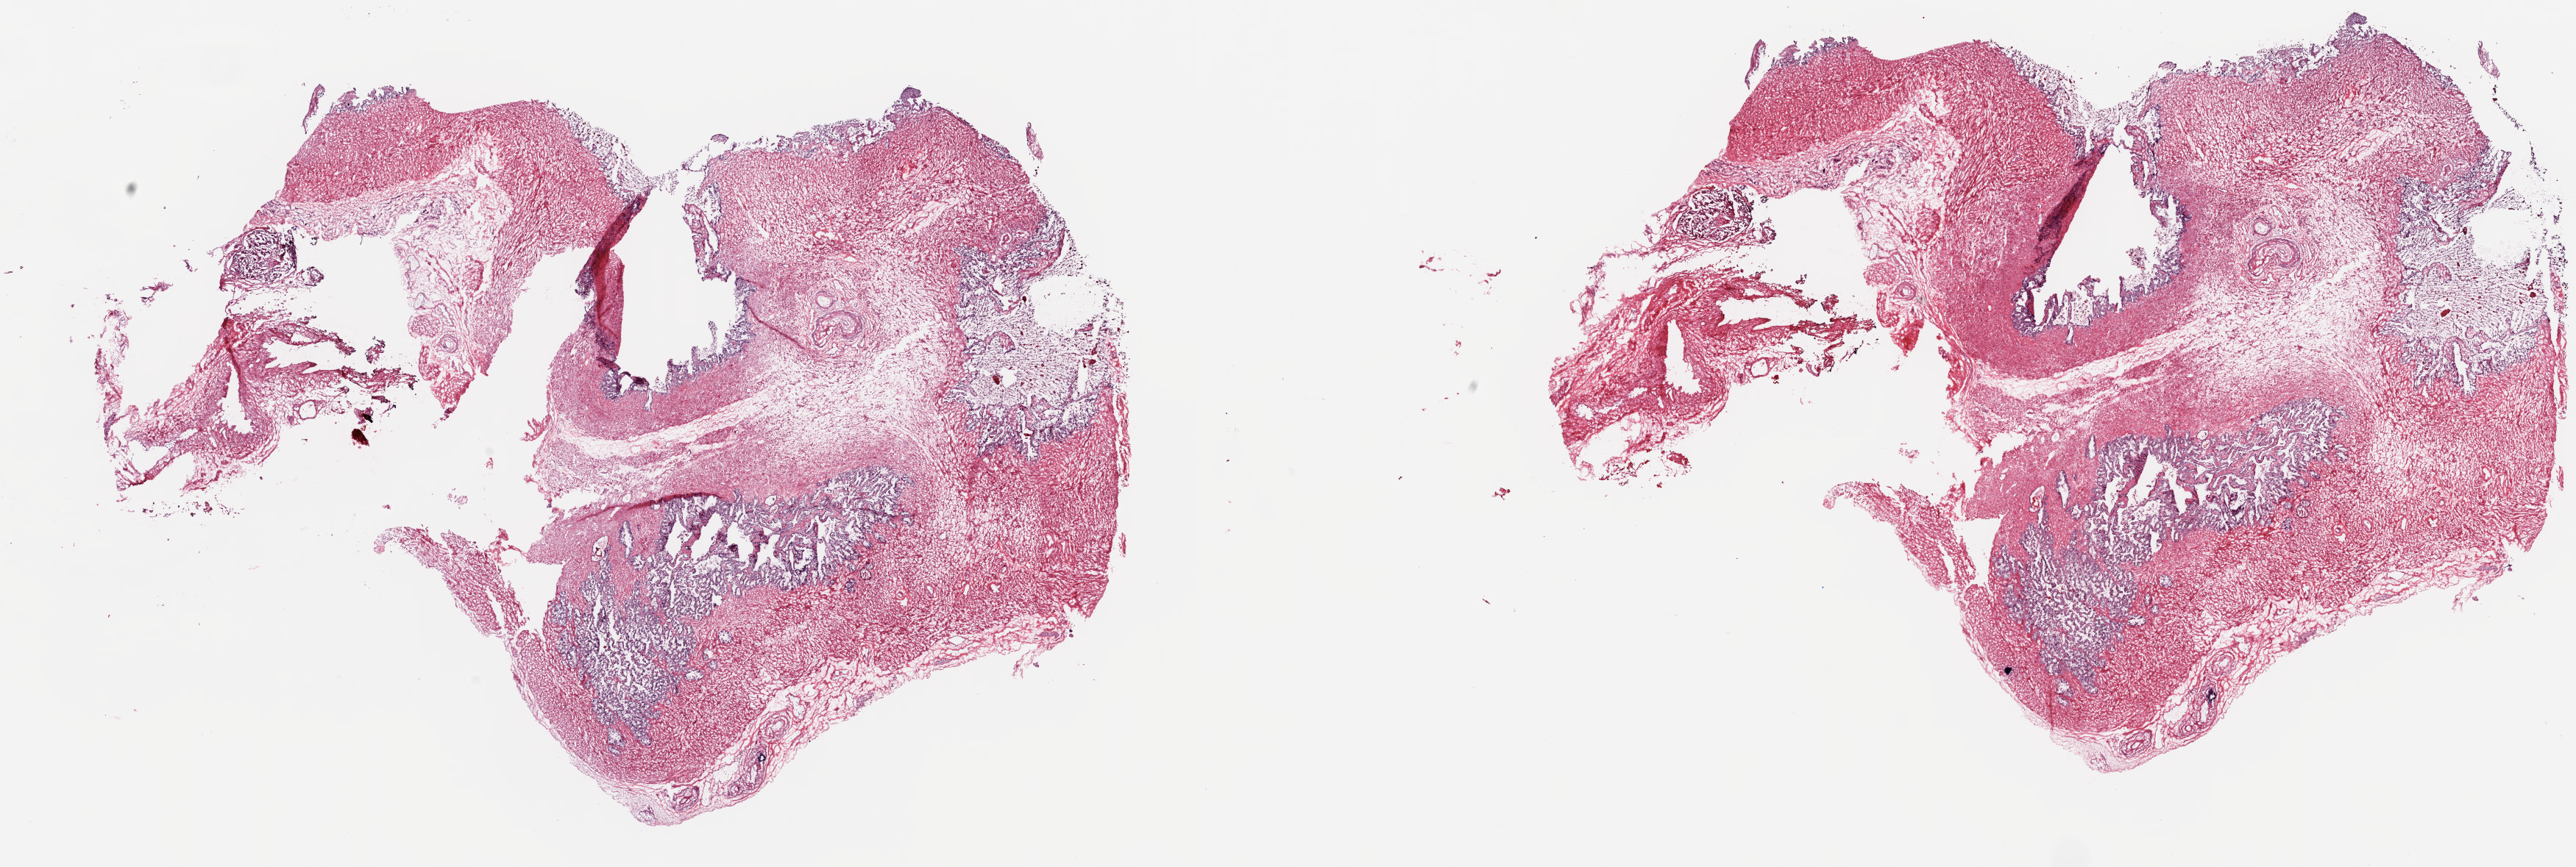
Whole-slide histology image, H&E-stained, whole scanned area (about 27.8 x 9.4 mm, from a 20x scan) shown as a low-resolution overview; frozen section from the top of the tissue portion; solid tissue normal (non-tumour tissue) sample from the prostate. Male patient; age at initial diagnosis 60 years. Slide review estimates, as recorded: tumour cells 0%, tumour nuclei 0%, normal cells 40%, stromal cells 60%, necrosis 0%. Inflammatory infiltration, as recorded: lymphocyte infiltration 70%, monocyte infiltration 10%, neutrophil infiltration 20%.
This section: solid tissue normal (non-tumour) sample from the same patient. Patient diagnosis: Adenocarcinoma, NOS (prostate gland).